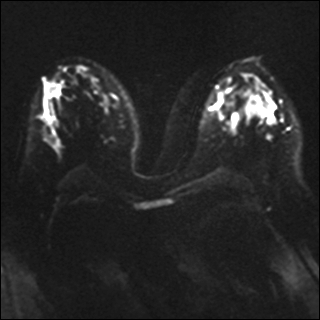
Breast MRI, one axial slice. Position 19 of 41 along the scan axis. Diffusion-weighted series; image 2 of 4 stored at this slice position (different b-values; order by instance number). 1.5 T. 4 mm slice thickness. 320 × 320 image matrix, field of view 340 × 340 mm. Female patient.
Outlined on this slice (outlined manually by an expert reader):
- tumour on diffusion-weighted imaging: bounding box <253,103,266,115> (left, top, right, bottom; pixels)